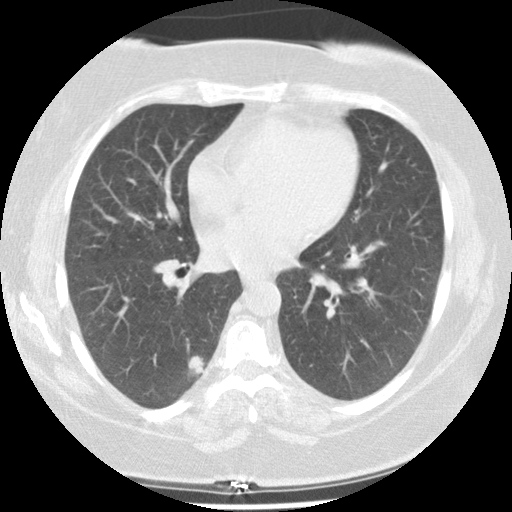
Low-dose screening chest CT, axial slice, second screening round (one year after baseline), lung window (W 1500 / L -600 HU), standard (soft-tissue) reconstruction kernel (STANDARD). Female participant, aged 58 years at enrolment.
Lesion marked by an expert reader, box from (x=162, y=332) to (x=221, y=398) px. The screening reader recorded 4 non-calcified nodules or masses ≥4 mm on this exam (right lower lobe, right middle lobe, right upper lobe, right middle lobe); which of them this box marks is not recorded. Lung cancer was diagnosed 299 days after this screen: adenocarcinoma, NOS, right lower lobe, stage IIIA (AJCC 6th edition), 25 mm at pathology.